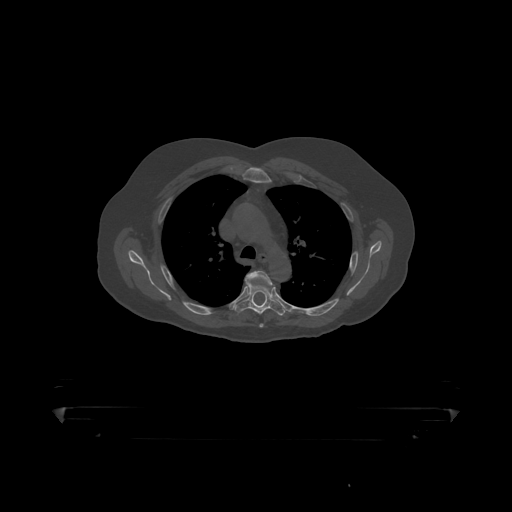
CT including the spine, one axial slice; reconstruction kernel STANDARD; 120 kVp; bone window (W 1800 / L 400 HU); 1.25 mm slice thickness; 512 × 512 image matrix, field of view 650 × 650 mm. Male patient, age 60 years. From the clinical record (not read from this slice): primary cancer: prostate.
Outlined on this slice (semi-automatically segmented with operator editing):
- T4 vertebra: box from (x=246, y=271) to (x=273, y=286) px
- T5 vertebra: (x=234, y=285)–(x=287, y=315)